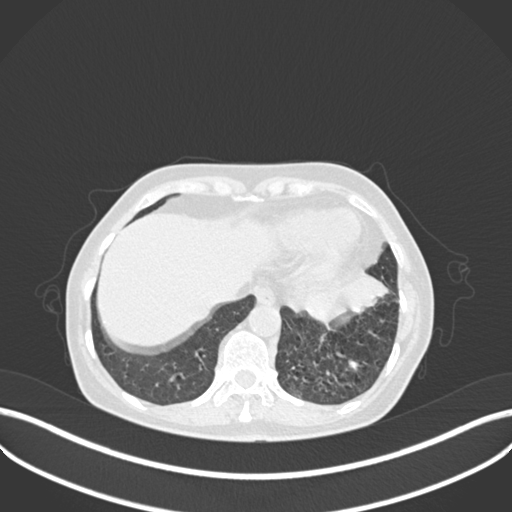
Chest CT, one axial slice. Position 52 of 270 along the scan axis. Reconstruction kernel B30f. Lung window (W 1500 / L -600 HU). 1 mm slice thickness. 512 × 512 image matrix, field of view 400 × 400 mm. Patient: female, 63 years. From the clinical record (not read from this slice): clinical TNM (as recorded): T1b N0 M0; histopathological grade: G2-3.
Annotated regions visible in this slice (rectangle marked by the reading radiologist):
- lung tumour (recorded histology: adenocarcinoma): box from (x=282, y=267) to (x=394, y=327) px